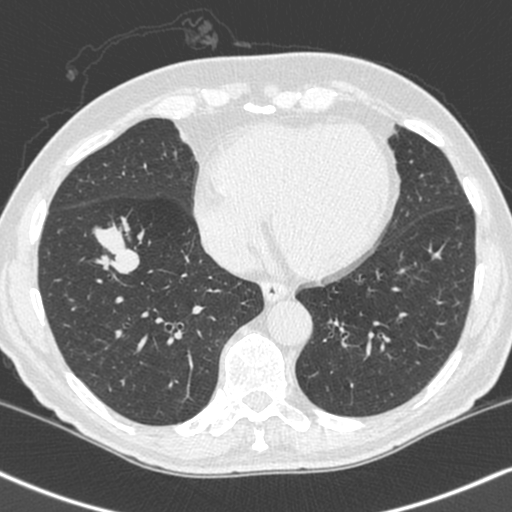
Chest CT (low-dose screening protocol), one axial image; baseline screening round; lung window (W 1500 / L -600 HU); 1.3 mm slice thickness; standard (soft-tissue) reconstruction kernel (C); 512 × 512 image matrix, field of view 323 × 323 mm. Male participant, aged 68 years at enrolment.
Expert reader's lesion annotation, box from (x=80, y=207) to (x=155, y=277) px. The exam's reader record, not a measurement of the box and not confirmed to be the same lesion: non-calcified nodule or mass ≥4 mm, right lower lobe, 34 × 17 mm, smooth margins, soft tissue attenuation. Lung cancer was diagnosed 24 days after this screen: combined small cell carcinoma, right lower lobe, stage IIIA (AJCC 6th edition), 41 mm at pathology.